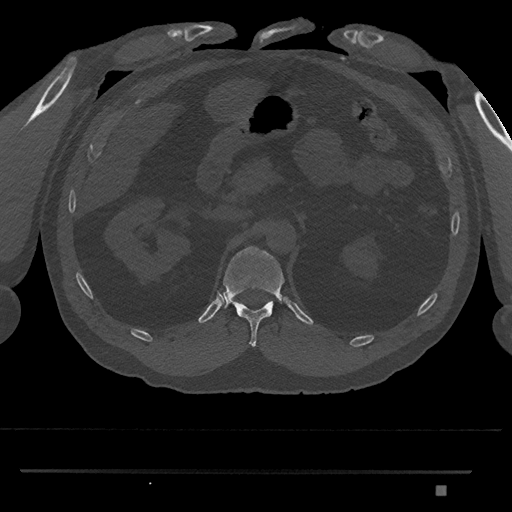
CT including the spine, one axial slice; slice 879 of 1134 in the series (ordered by position); reconstruction kernel Br40s/3; 120 kVp; bone window (W 1800 / L 400 HU); 512 × 512 image matrix, field of view 429 × 429 mm. Patient: male, 65 years. From the clinical record (not read from this slice): primary cancer: prostate.
Annotated regions visible in this slice (semi-automatic segmentation, software-assisted and operator-edited):
- T12 vertebra: bounding box (x1, y1, x2, y2) in pixels: (220, 246, 285, 347)